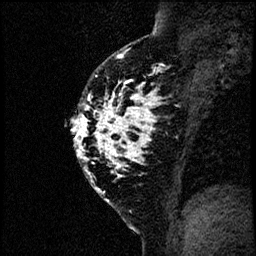
Breast MRI (dynamic contrast-enhanced), one sagittal slice. Slice 43 of 60 in the series (ordered by position). Dynamic contrast-enhanced study with each time point stored as its own series, time point 2 of 4 at this slice position (early post-contrast, ordered by acquisition time). 1.5 T. TE 4.2 ms, TR 17.6 ms. 2 mm slice thickness. 256 × 256 image matrix. Female patient, age 40 years. From the clinical record (not read from this slice): setting: breast cancer imaged before/during neoadjuvant chemotherapy; receptor status: HER2-positive.
Annotated regions visible in this slice (semi-automatic segmentation, software-assisted and operator-edited):
- analysis volume of interest (the breast-tissue region the enhancement analysis was run in; not a lesion): bounding box [x1, y1, x2, y2] px = [67, 55, 185, 206]
- tumour enhancement mask (voxels above the 100 % enhancement threshold inside the analysis volume of interest): [70, 55, 157, 170]